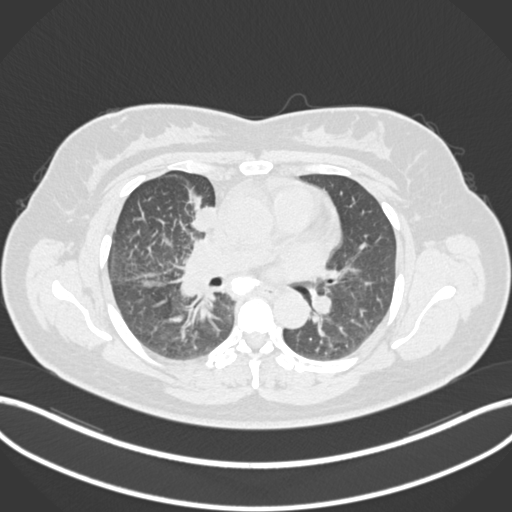
Chest CT, one axial slice; slice 94 of 183 in the series (ordered by position); 120 kVp; lung window (W 1500 / L -600 HU); 1 mm slice thickness; 512 × 512 image matrix, field of view 400 × 400 mm. Female patient, age 46 years. From the clinical record (not read from this slice): clinical TNM (as recorded): T2a N1 M0.
Structures marked on this image (bounding box drawn by a radiologist):
- lung tumour (recorded histology: adenocarcinoma): box from (x=186, y=194) to (x=216, y=238) px